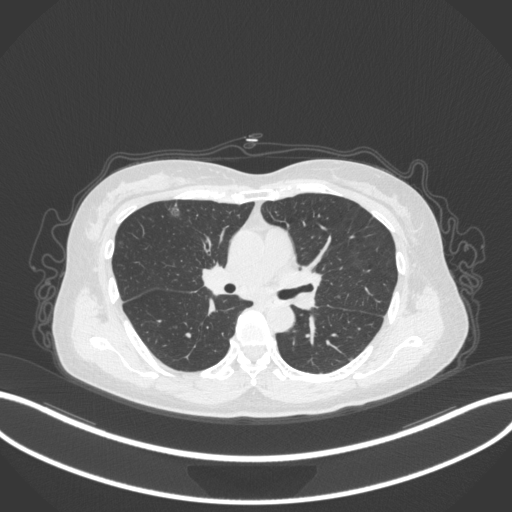
Chest CT, one axial slice. Position 193 of 317 along the scan axis. Lung window (W 1500 / L -600 HU). 512 × 512 image matrix, field of view 400 × 400 mm. Female patient, age 61 years. Case-level facts recorded for this patient, not image findings: clinical TNM (as recorded): T1b N0 M0.
Outlined on this slice (rectangle marked by the reading radiologist):
- lung tumour (recorded histology: adenocarcinoma): box from (x=165, y=200) to (x=183, y=221) px